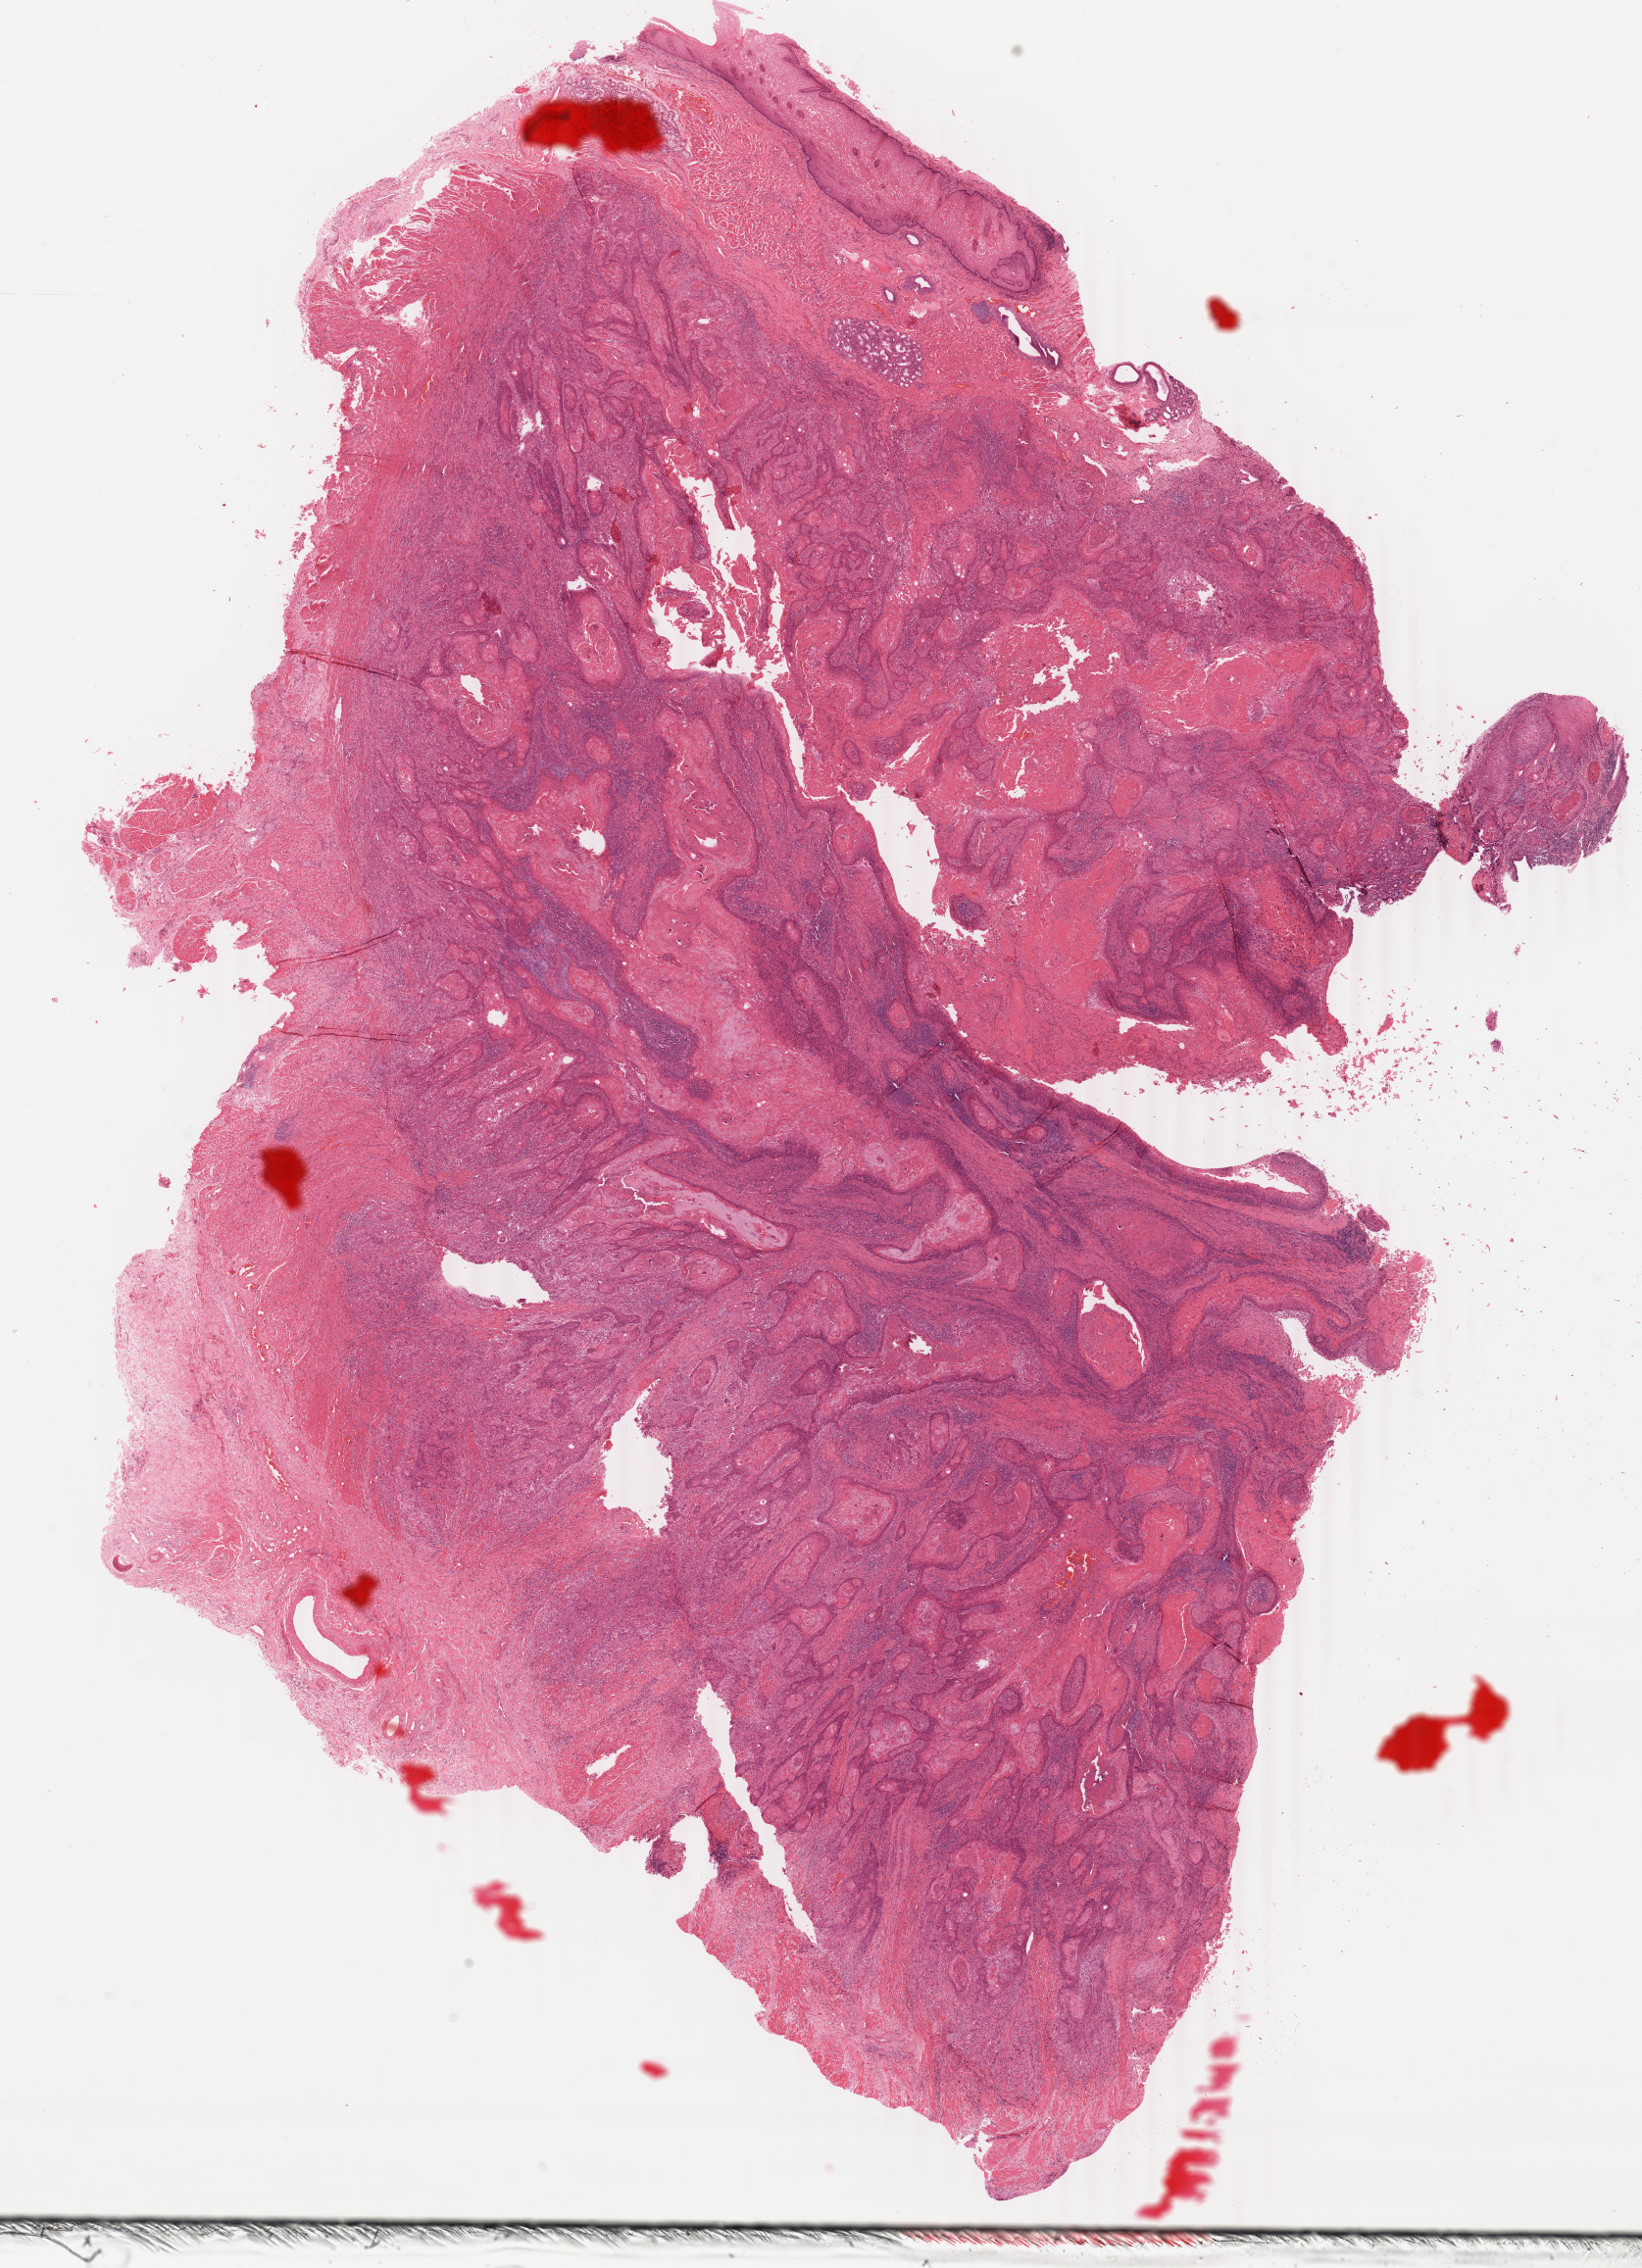
Hematoxylin and eosin (H&E) stained whole-slide image, whole scanned area (about 13.3 x 18.4 mm) shown as a low-resolution overview; formalin-fixed paraffin-embedded (FFPE) diagnostic section; primary tumour sample from the esophagus. Male patient; age at initial diagnosis 72 years. Histologic grade: G1 (well differentiated).
• AJCC pathologic stage: IB
• pathologic diagnosis: Squamous cell carcinoma, keratinizing, NOS
• lymph nodes positive (case pathology): 0 of 1 examined